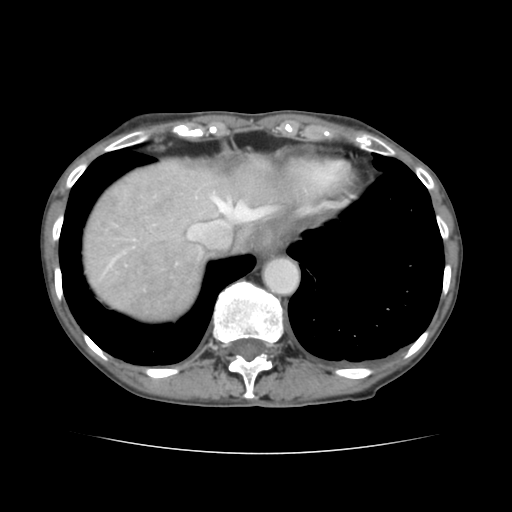
Contrast-enhanced abdominal CT, one axial slice. Position 123 of 136 along the scan axis. 120 kVp. Intravenous contrast given. Soft-tissue window (W 400 / L 40 HU). 2.5 mm slice thickness. 512 × 512 image matrix, field of view 319 × 319 mm. Female patient, age 77 years. Case-level facts recorded for this patient, not image findings: diagnosis: colorectal cancer liver metastases, imaged before liver resection; multiple liver metastases: yes; largest metastasis: 3 cm; disease in both lobes: no.
Structures marked on this image (manually delineated by an expert):
- hepatic veins: box from (x=109, y=191) to (x=272, y=264) px
- liver: (x=83, y=157)–(x=289, y=320)
- planned liver remnant (the part of the liver to remain after resection): (x=183, y=156)–(x=290, y=245)